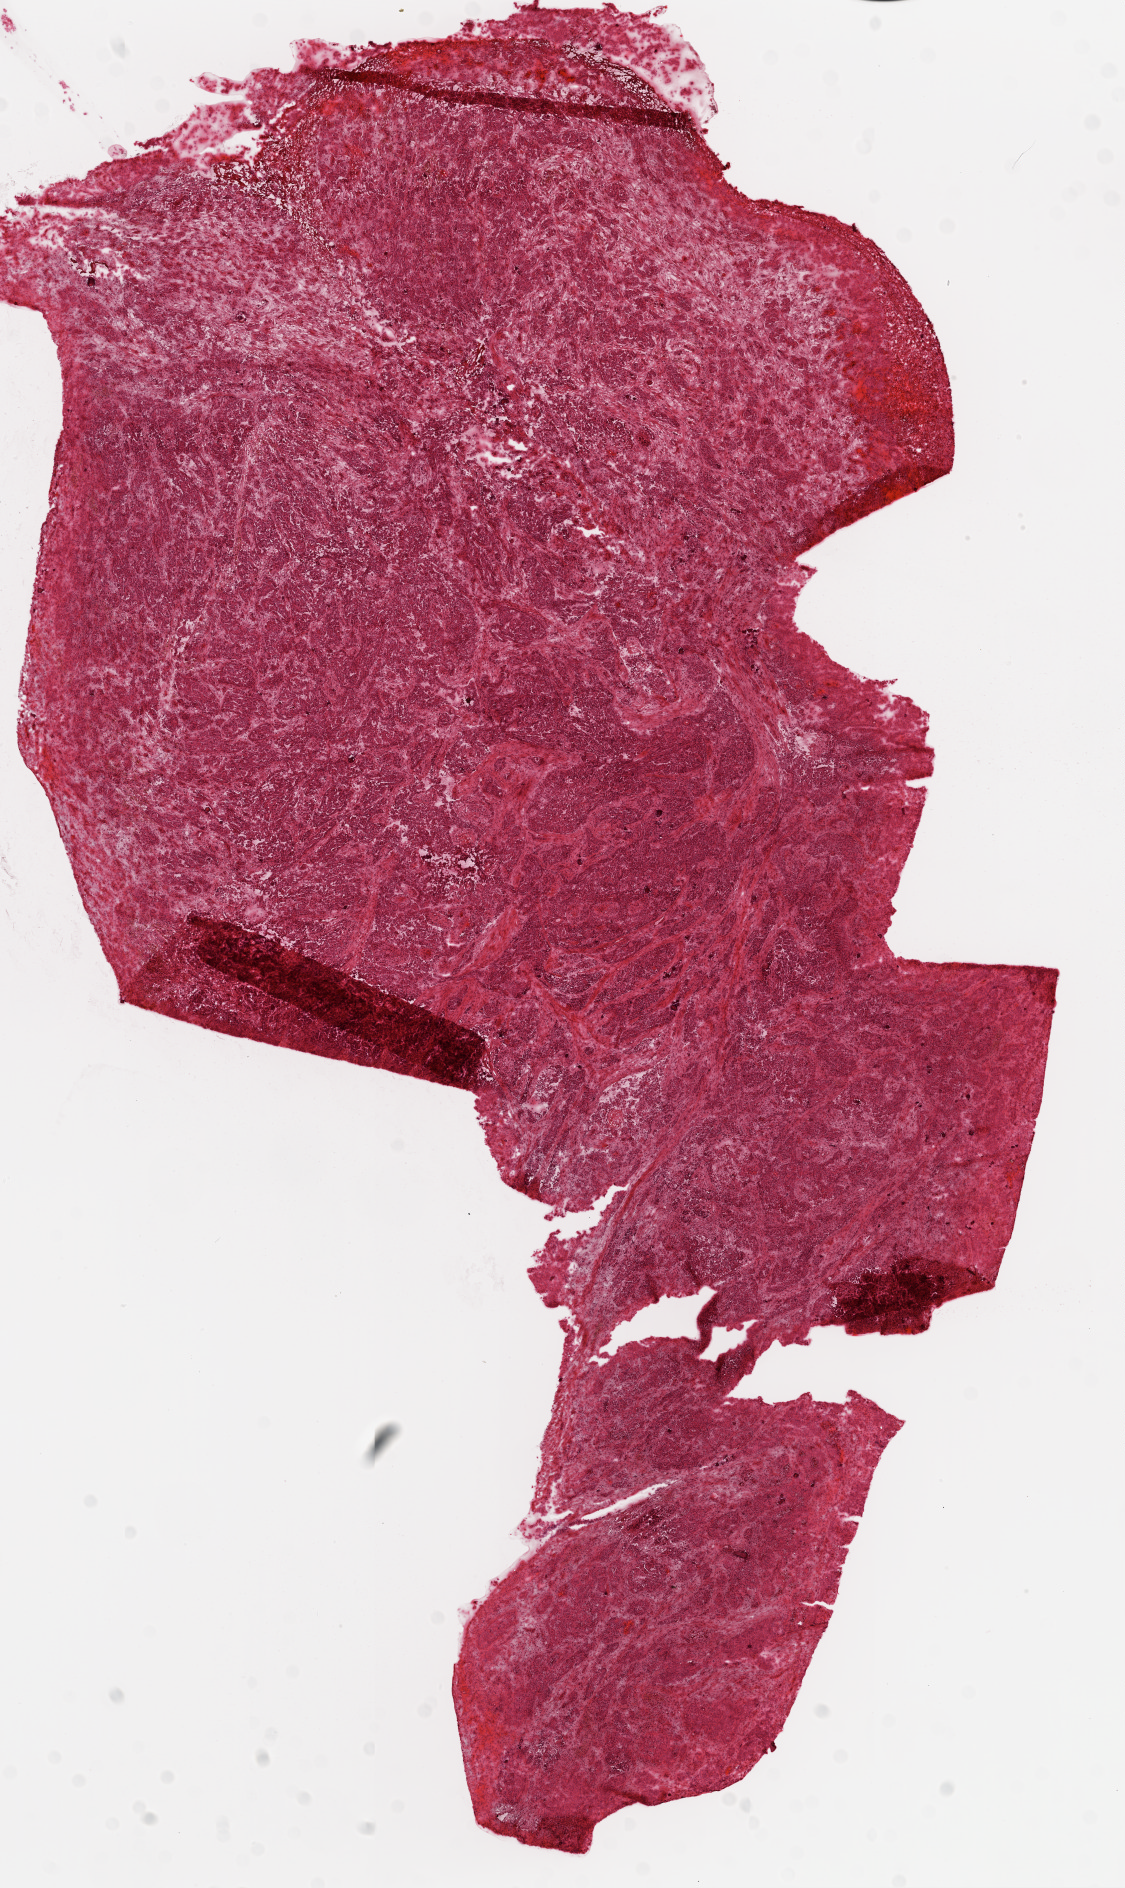
Hematoxylin and eosin (H&E) stained whole-slide image, low-resolution overview of the scanned area, about 9.0 x 15.1 mm, frozen section from the top of the tissue portion, primary tumour sample from the ovary. Patient: female, age at initial diagnosis 82 years. Histologic grade: G3 (poorly differentiated). Slide review estimates, as recorded: tumour cells 50%, tumour nuclei 90%, normal cells 40%, stromal cells 0%, necrosis 10%.
• FIGO stage: IIIC
• diagnosis: Serous cystadenocarcinoma, NOS